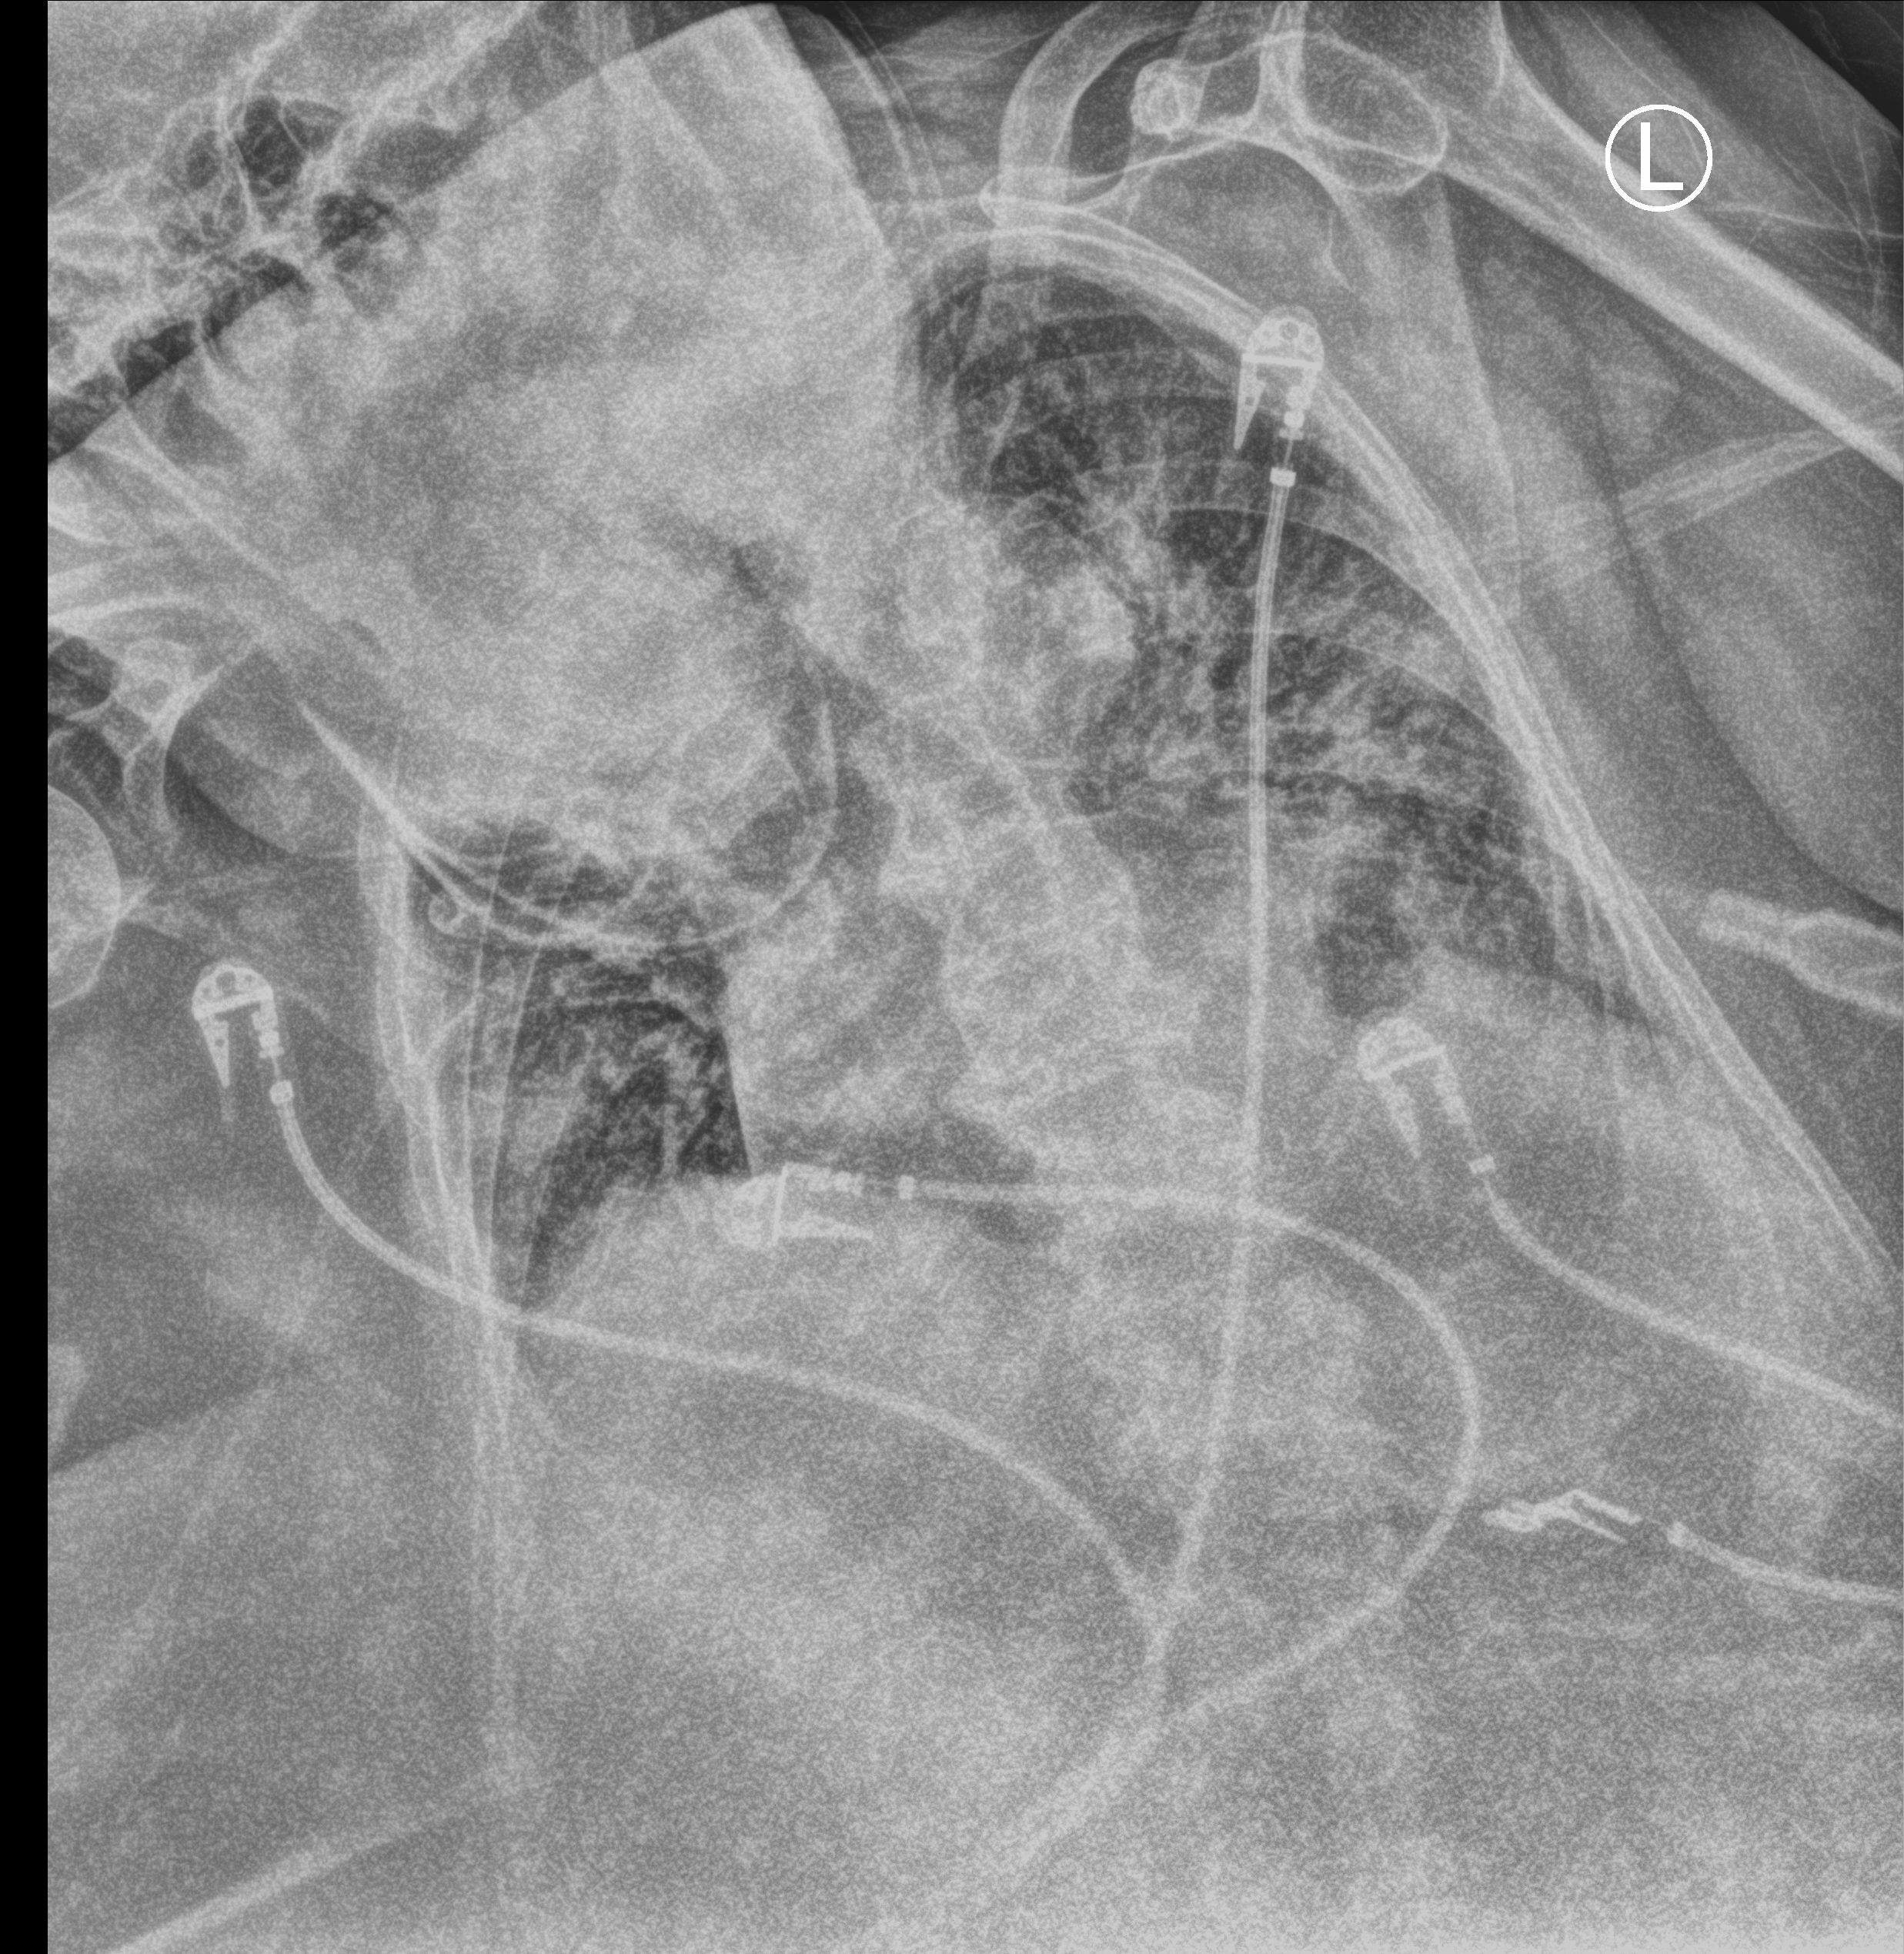
Portable chest radiograph. Patient hospitalised with COVID-19; female, aged 75–90 years.
Hospital-stay facts (about this admission, not read from this image; timing relative to this image not recorded): admitted to intensive care during this hospital stay: no; mechanically ventilated during this hospital stay: no.